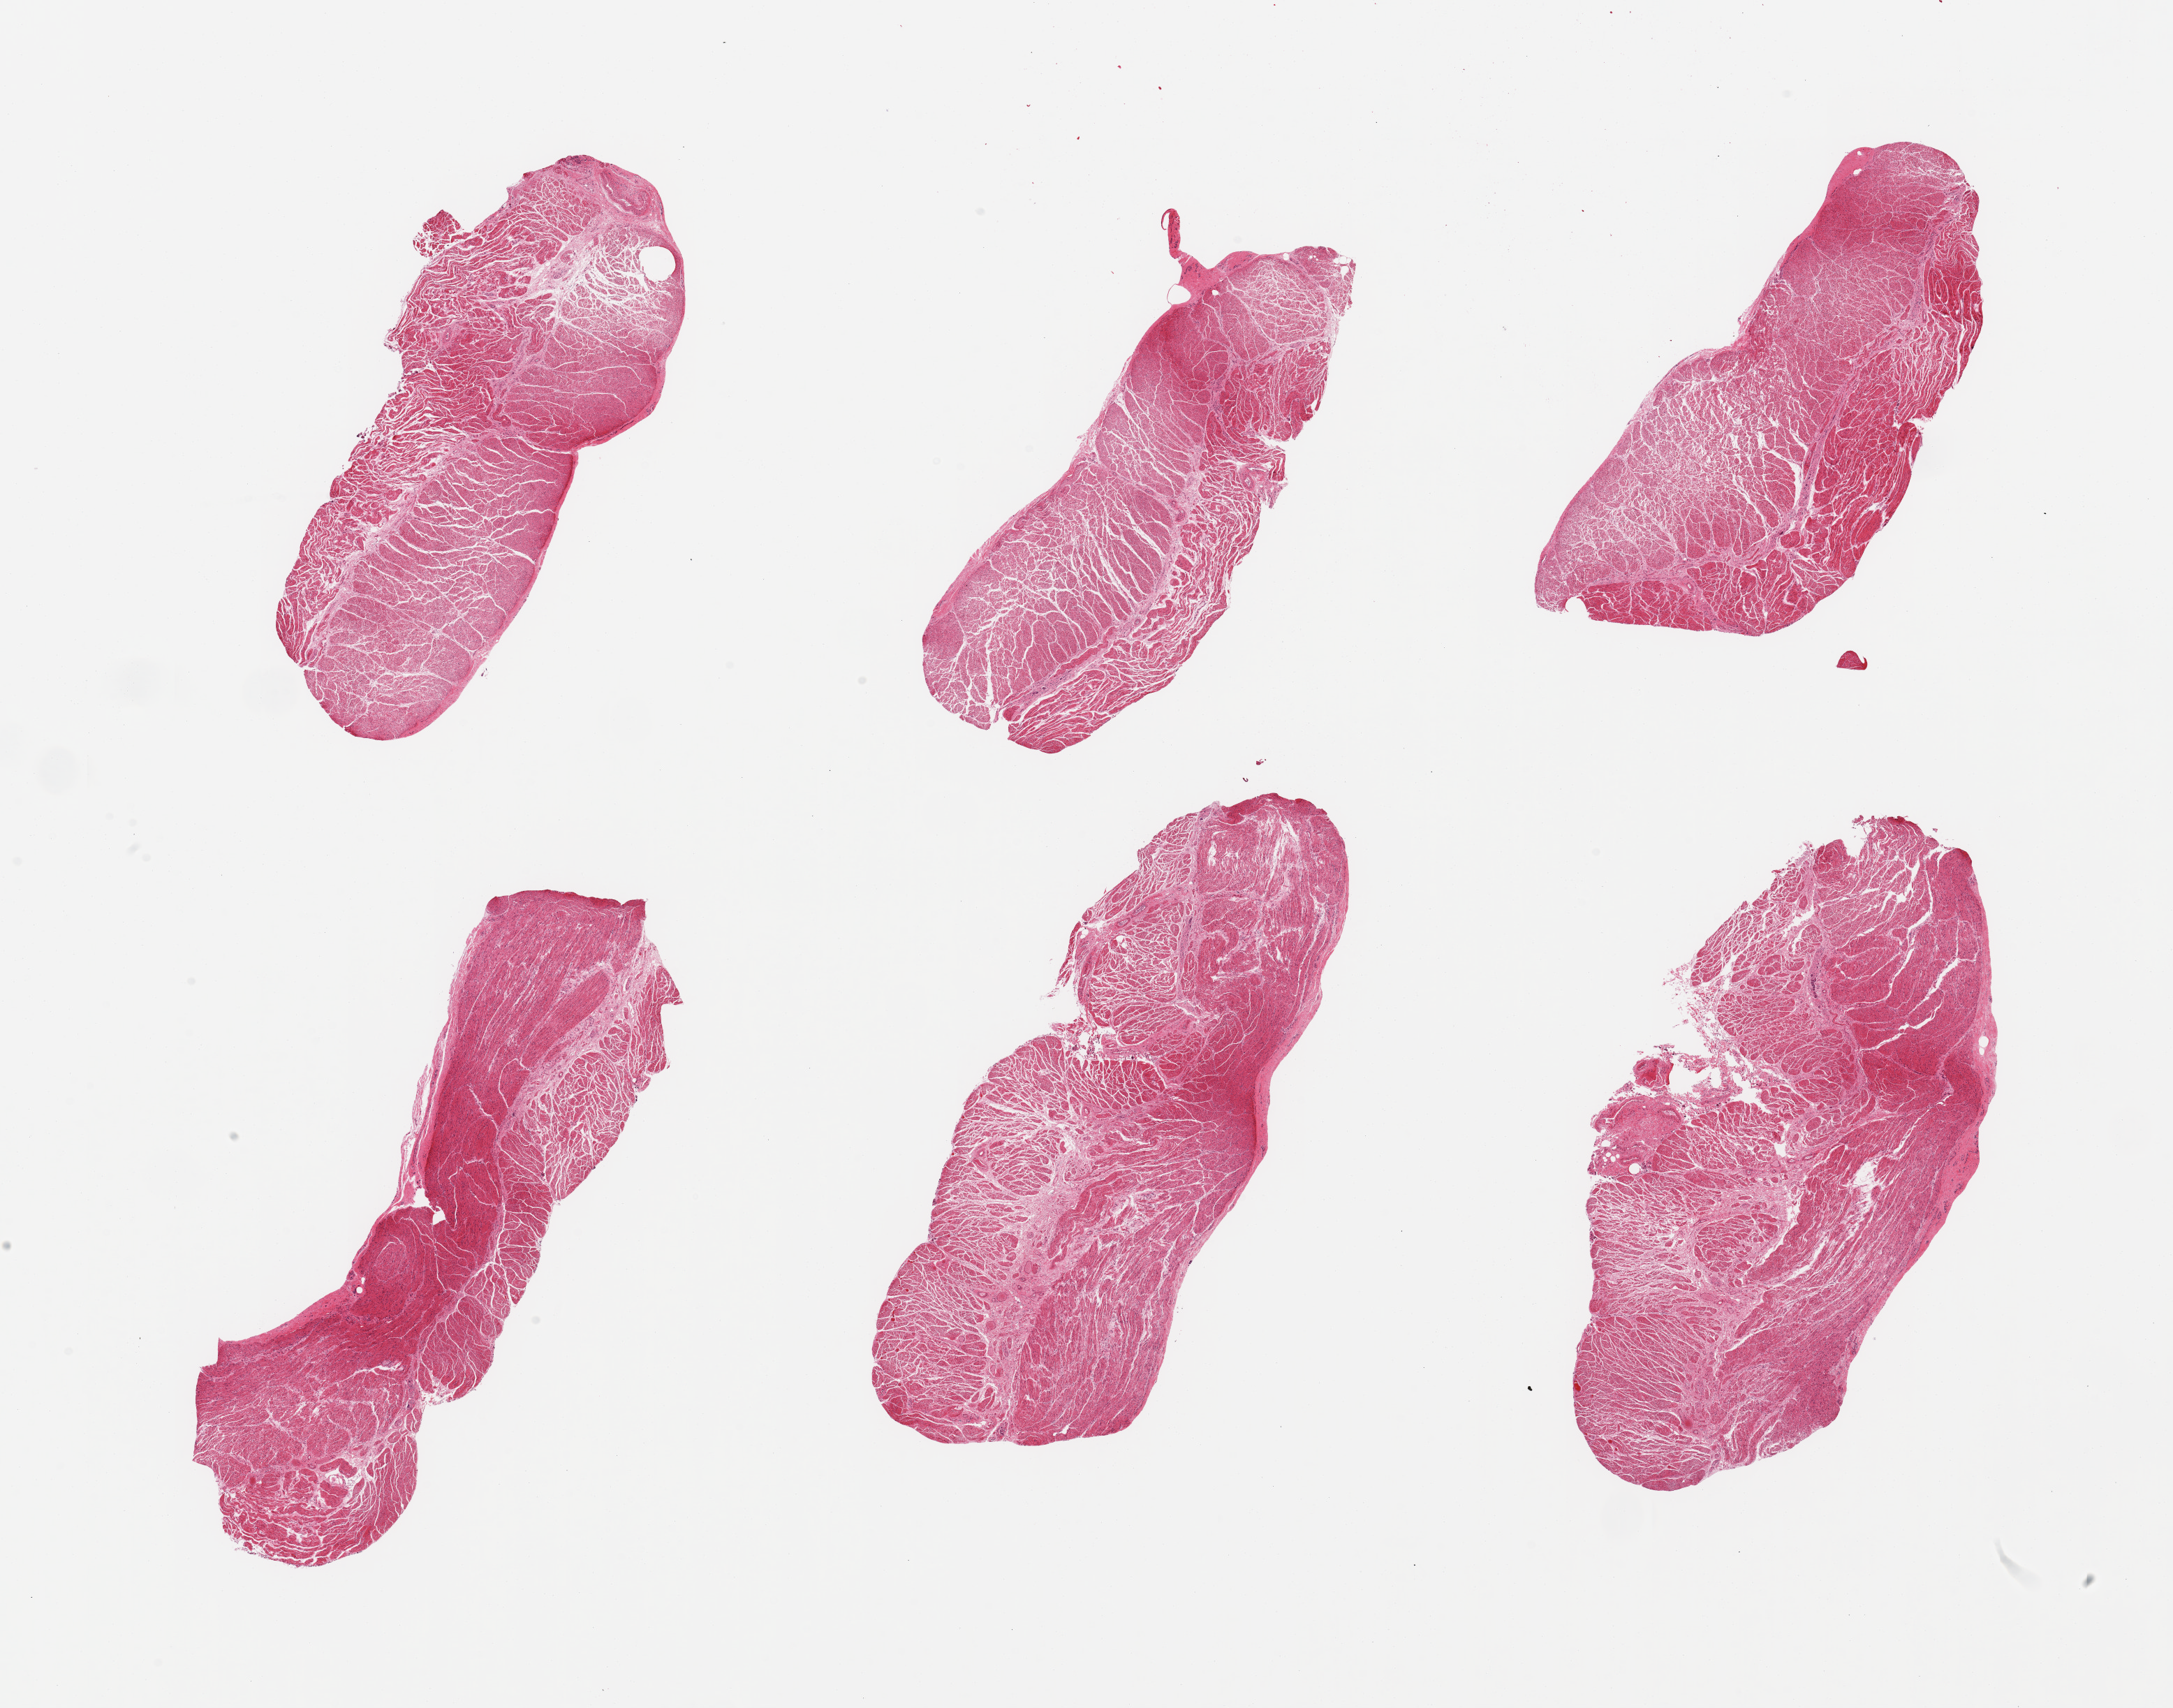
Hematoxylin and eosin (H&E) whole-slide image, brightfield, shown as a low-resolution overview of the whole scanned area (about 24.6 x 19.3 mm); PAXgene-fixed, paraffin-embedded tissue; section of esophageal muscle (target tissue); tissue donor sample. Donor sex: male.
Reviewer comment on this tissue sample: 6 pieces; target muscularis.